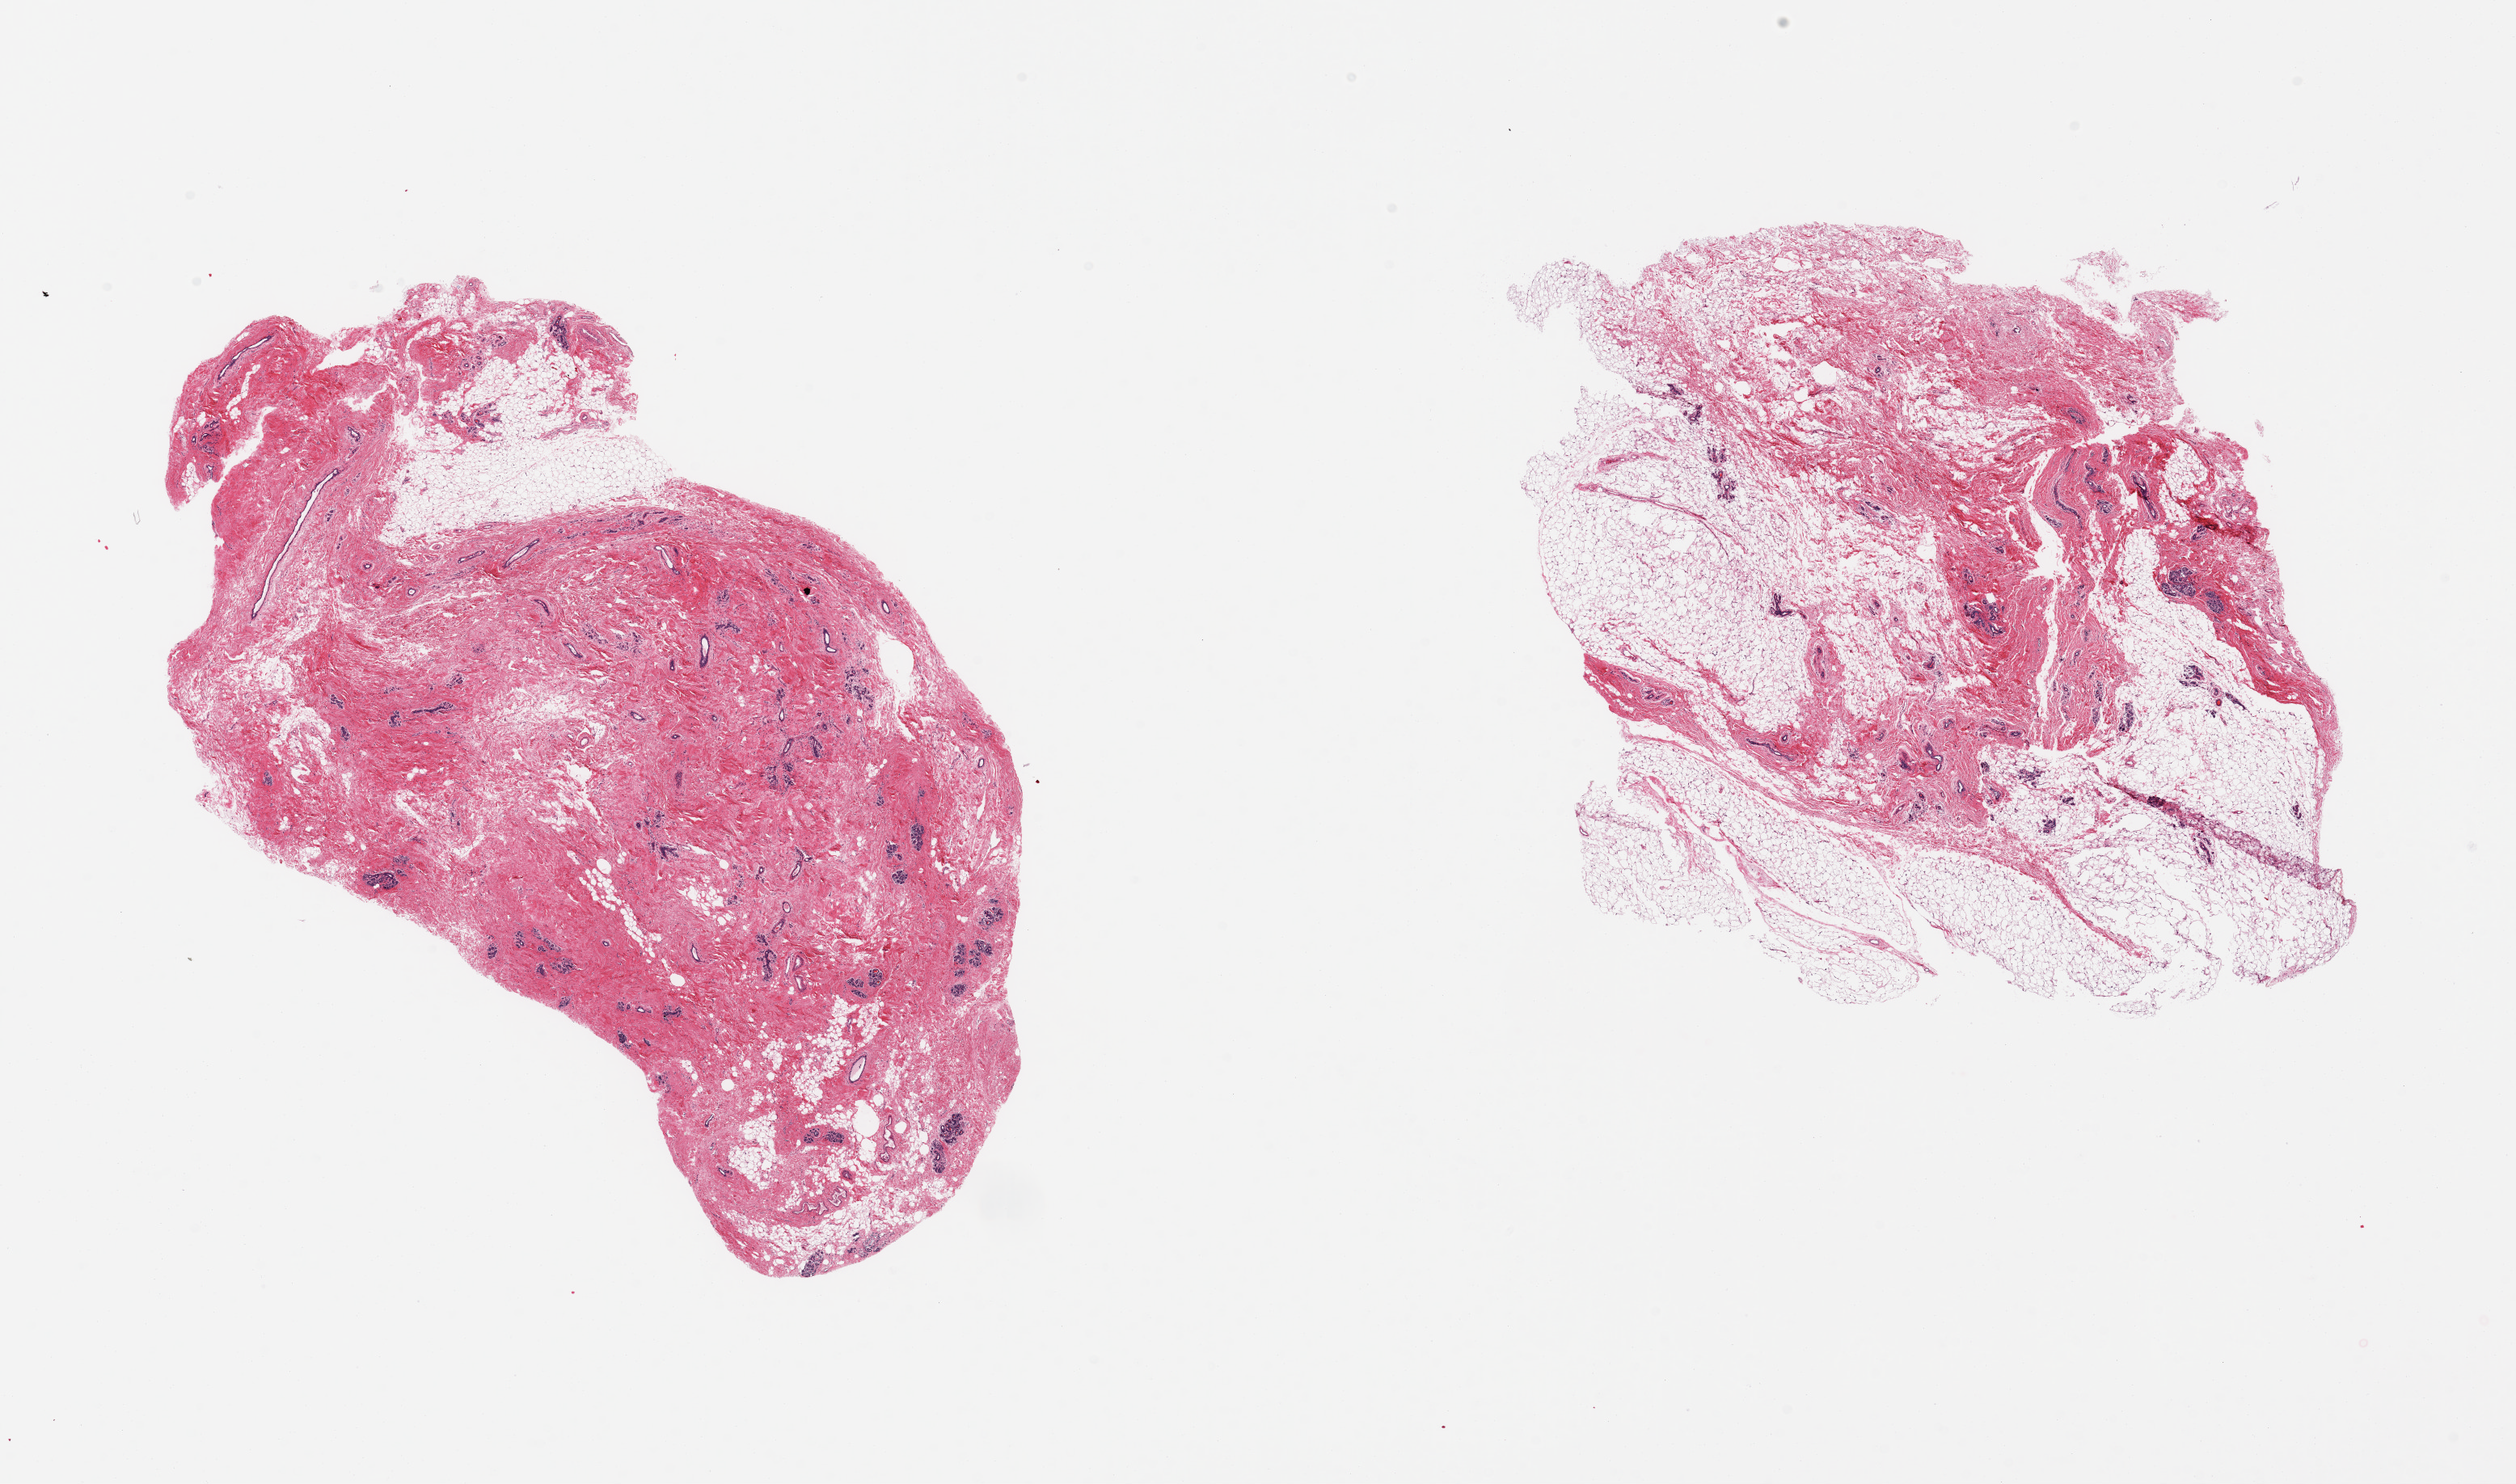
Hematoxylin and eosin (H&E) whole-slide image, brightfield, low-resolution overview of the scanned area, about 24.6 x 14.5 mm; PAXgene-fixed paraffin-embedded (PFPE) section; section of breast (target tissue); tissue donor sample. Female donor.
* reviewer comment on this tissue sample: 2 pieces; ductal and lobular units present in a fibrofatty stroma